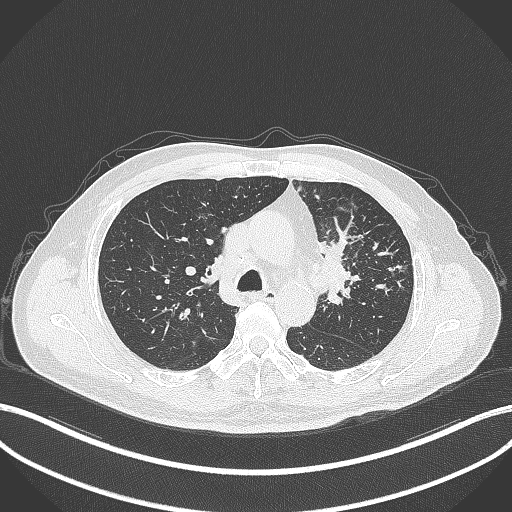
Chest CT, one axial slice; slice 236 of 386 in the series (ordered by position); lung window (W 1500 / L -600 HU); 1 mm slice thickness; 512 × 512 image matrix, field of view 400 × 400 mm. Male patient, age 69 years. From the clinical record (not read from this slice): clinical TNM (as recorded): T2a N2 M0.
Annotated regions visible in this slice (rectangle marked by the reading radiologist):
- lung tumour (recorded histology: adenocarcinoma): bounding box [x1, y1, x2, y2] px = [317, 234, 357, 311]